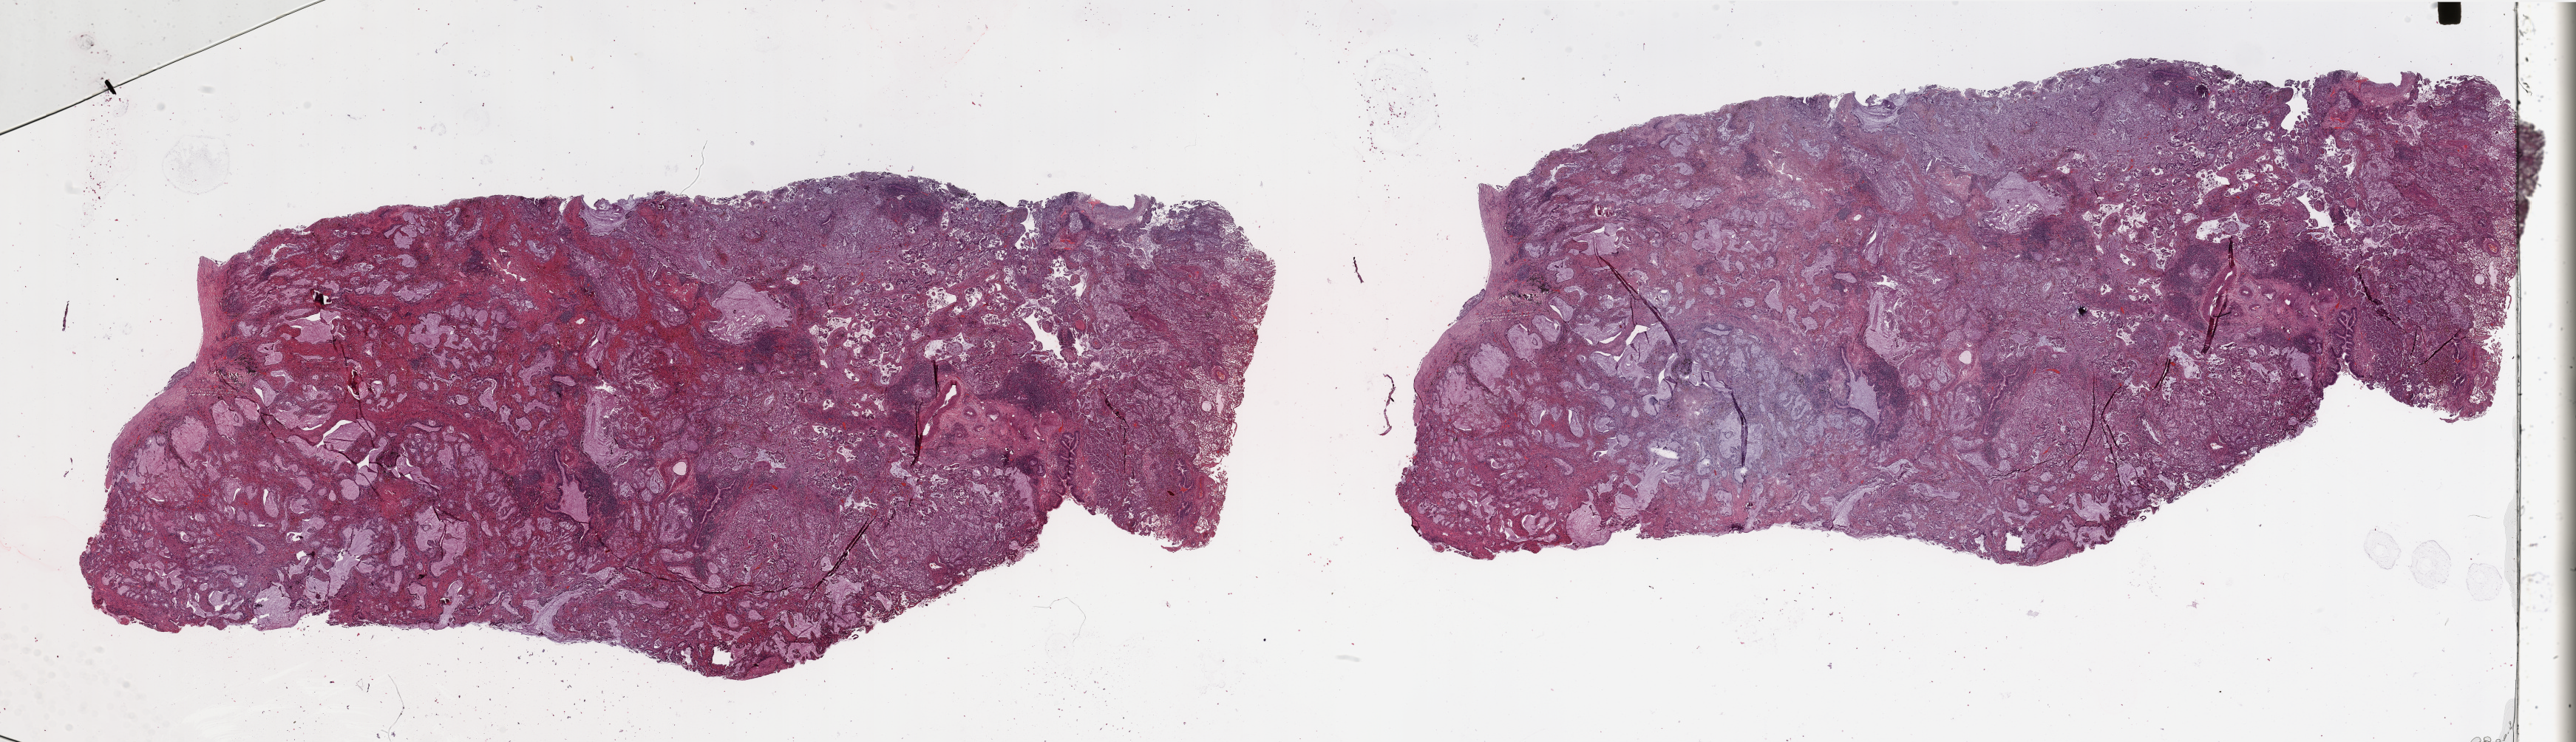
Whole-slide histology image, H&E, a low-resolution overview of the entire scanned area, about 55.1 x 15.9 mm (acquisition: 20x scan), tumour tissue sample, sampled site: lung. 64-year-old male patient. Histologic grade: G2 (moderately differentiated). Slide review estimates, as recorded: tumour nuclei 75%, necrosis 5%.
Primary tumour site (as recorded): left lower lobe. AJCC pathologic stage: IIA. Diagnosis: Adenocarcinoma, NOS.